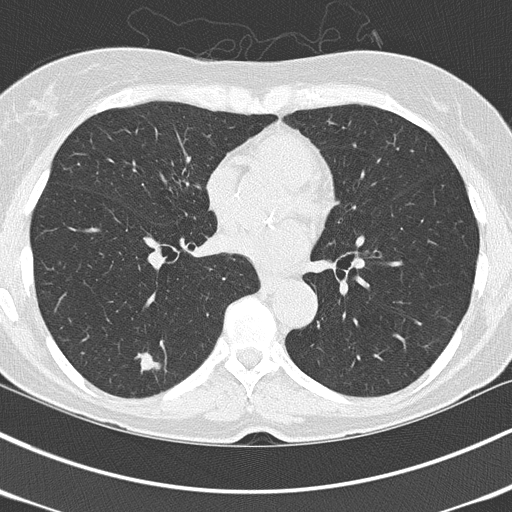
Chest CT (low-dose screening protocol), one axial image; third annual screen; lung window (W 1500 / L -600 HU). Female, age 67 years at enrolment. Current smoker at enrolment.
Expert reader's lesion annotation, bounding box (x1, y1, x2, y2) in pixels: (128, 347, 167, 383). The screening reader recorded 3 non-calcified nodules or masses ≥4 mm on this exam (right lower lobe, right lower lobe, left lower lobe); which of them this box marks is not recorded. Participant outcome: lung cancer diagnosed 64 days after this screen — adenocarcinoma, NOS, left lower lobe, poorly differentiated (G3), stage IA (AJCC 6th edition), 25 mm at pathology.